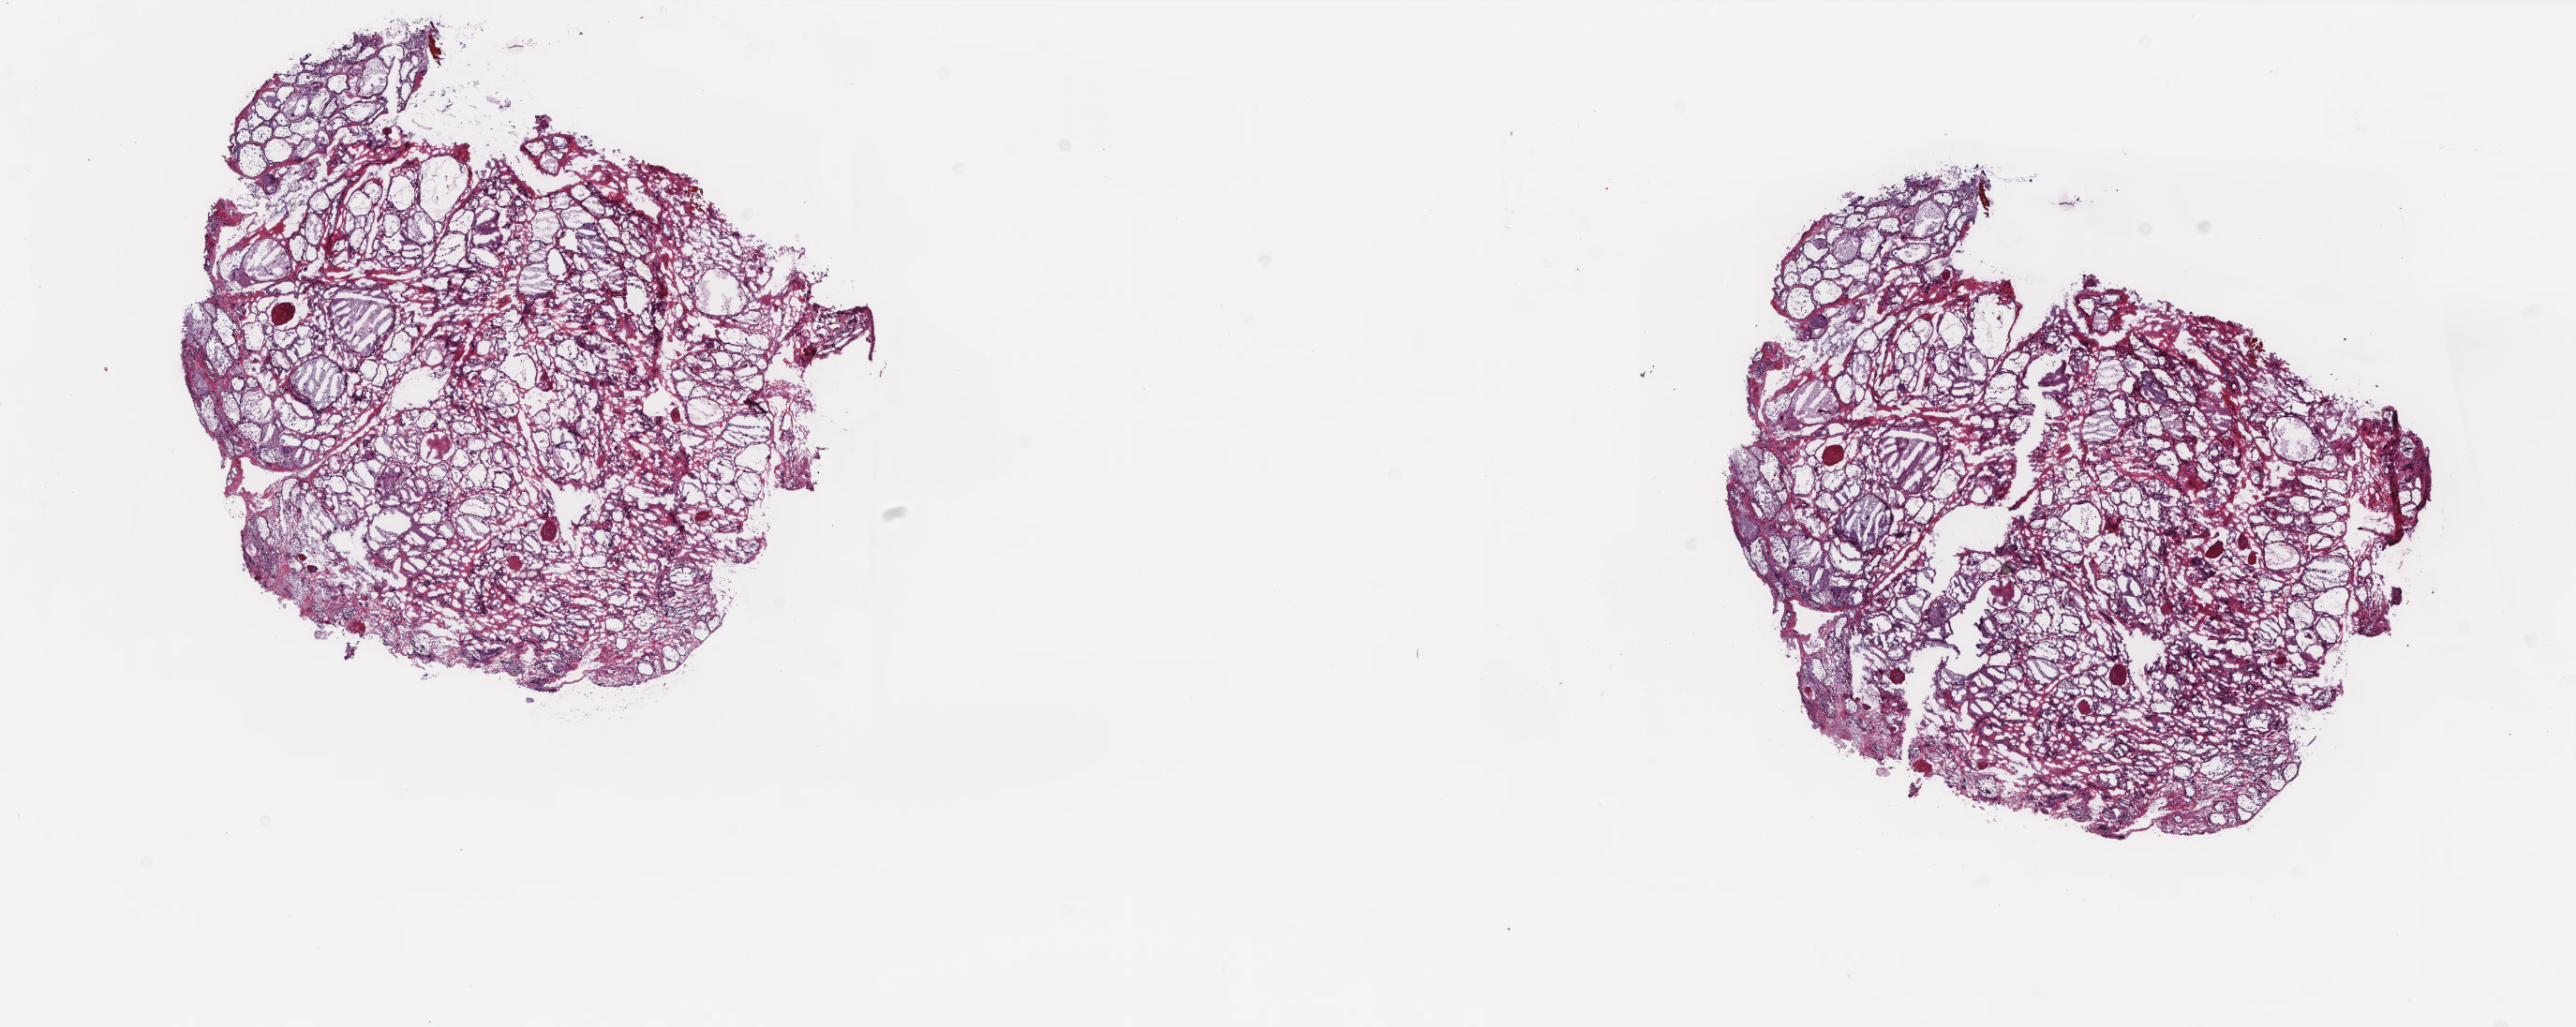
Whole-slide histology image, Hematoxylin and eosin (H&E) stained, shown as a low-resolution overview of the whole scanned area (about 22.0 x 8.8 mm, slide scanned at 20x), frozen section, solid tissue normal (non-tumour tissue) sample from the thyroid. Patient: male, age at initial diagnosis 63 years. Pathologist review of this section (percent, as recorded): tumour cells 0%, tumour nuclei 0%, normal cells 100%, stromal cells 0%, necrosis 0%. Inflammatory infiltration, as recorded: lymphocyte infiltration 0%, monocyte infiltration 2%, neutrophil infiltration 0%.
* this section: solid tissue normal (non-tumour) sample from the same patient
* patient diagnosis: Papillary adenocarcinoma, NOS (thyroid gland)